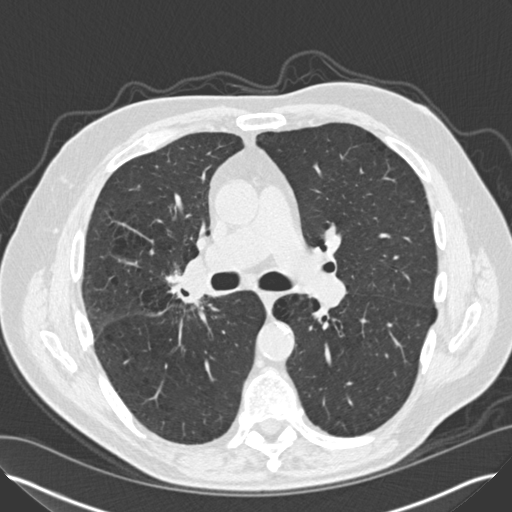
Axial slice from a low-dose chest CT screening exam; second screening round (one year after baseline); lung window (W 1500 / L -600 HU); 2 mm slice thickness. Male, age 65 years at enrolment. Current smoker at enrolment.
- Expert reader's lesion annotation, bounding box [x1, y1, x2, y2] px = [159, 262, 216, 315].
- Reader record for this screening exam (exam-level; its link to the box is not recorded): non-calcified nodule or mass ≥4 mm, left lower lobe, 12 × 8 mm, smooth margins, soft tissue attenuation, pre-existing on the prior screen: yes; interval growth: yes.
- Note: the box lies in the patient's right hemithorax on this image, whereas the reader's record names the left lung; they may be different findings.
- Later outcome: lung cancer diagnosed 67 days after this screen — non-small cell carcinoma, left lower lobe, right hilum, poorly differentiated (G3), stage IV (AJCC 6th edition), 5 mm at pathology.